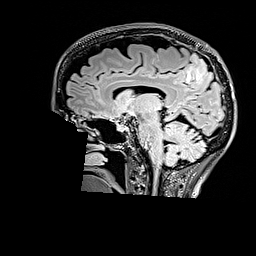
Brain MRI from a brain-tumour surgery series, one sagittal slice. Slice 98 of 176 in the series (ordered by position). T2 FLAIR. 1 mm slice thickness. 256 × 256 image matrix, field of view 256 × 256 mm. Case-level facts recorded for this patient, not image findings: histopathology: Astrocytoma; WHO grade: 3; IDH mutation: yes; tumour location: Right Parietal.
Outlined on this slice (outlined manually by an expert reader):
- tumour: bounding box <183,56,211,82> (left, top, right, bottom; pixels)
- tumour: <185,54,214,82>